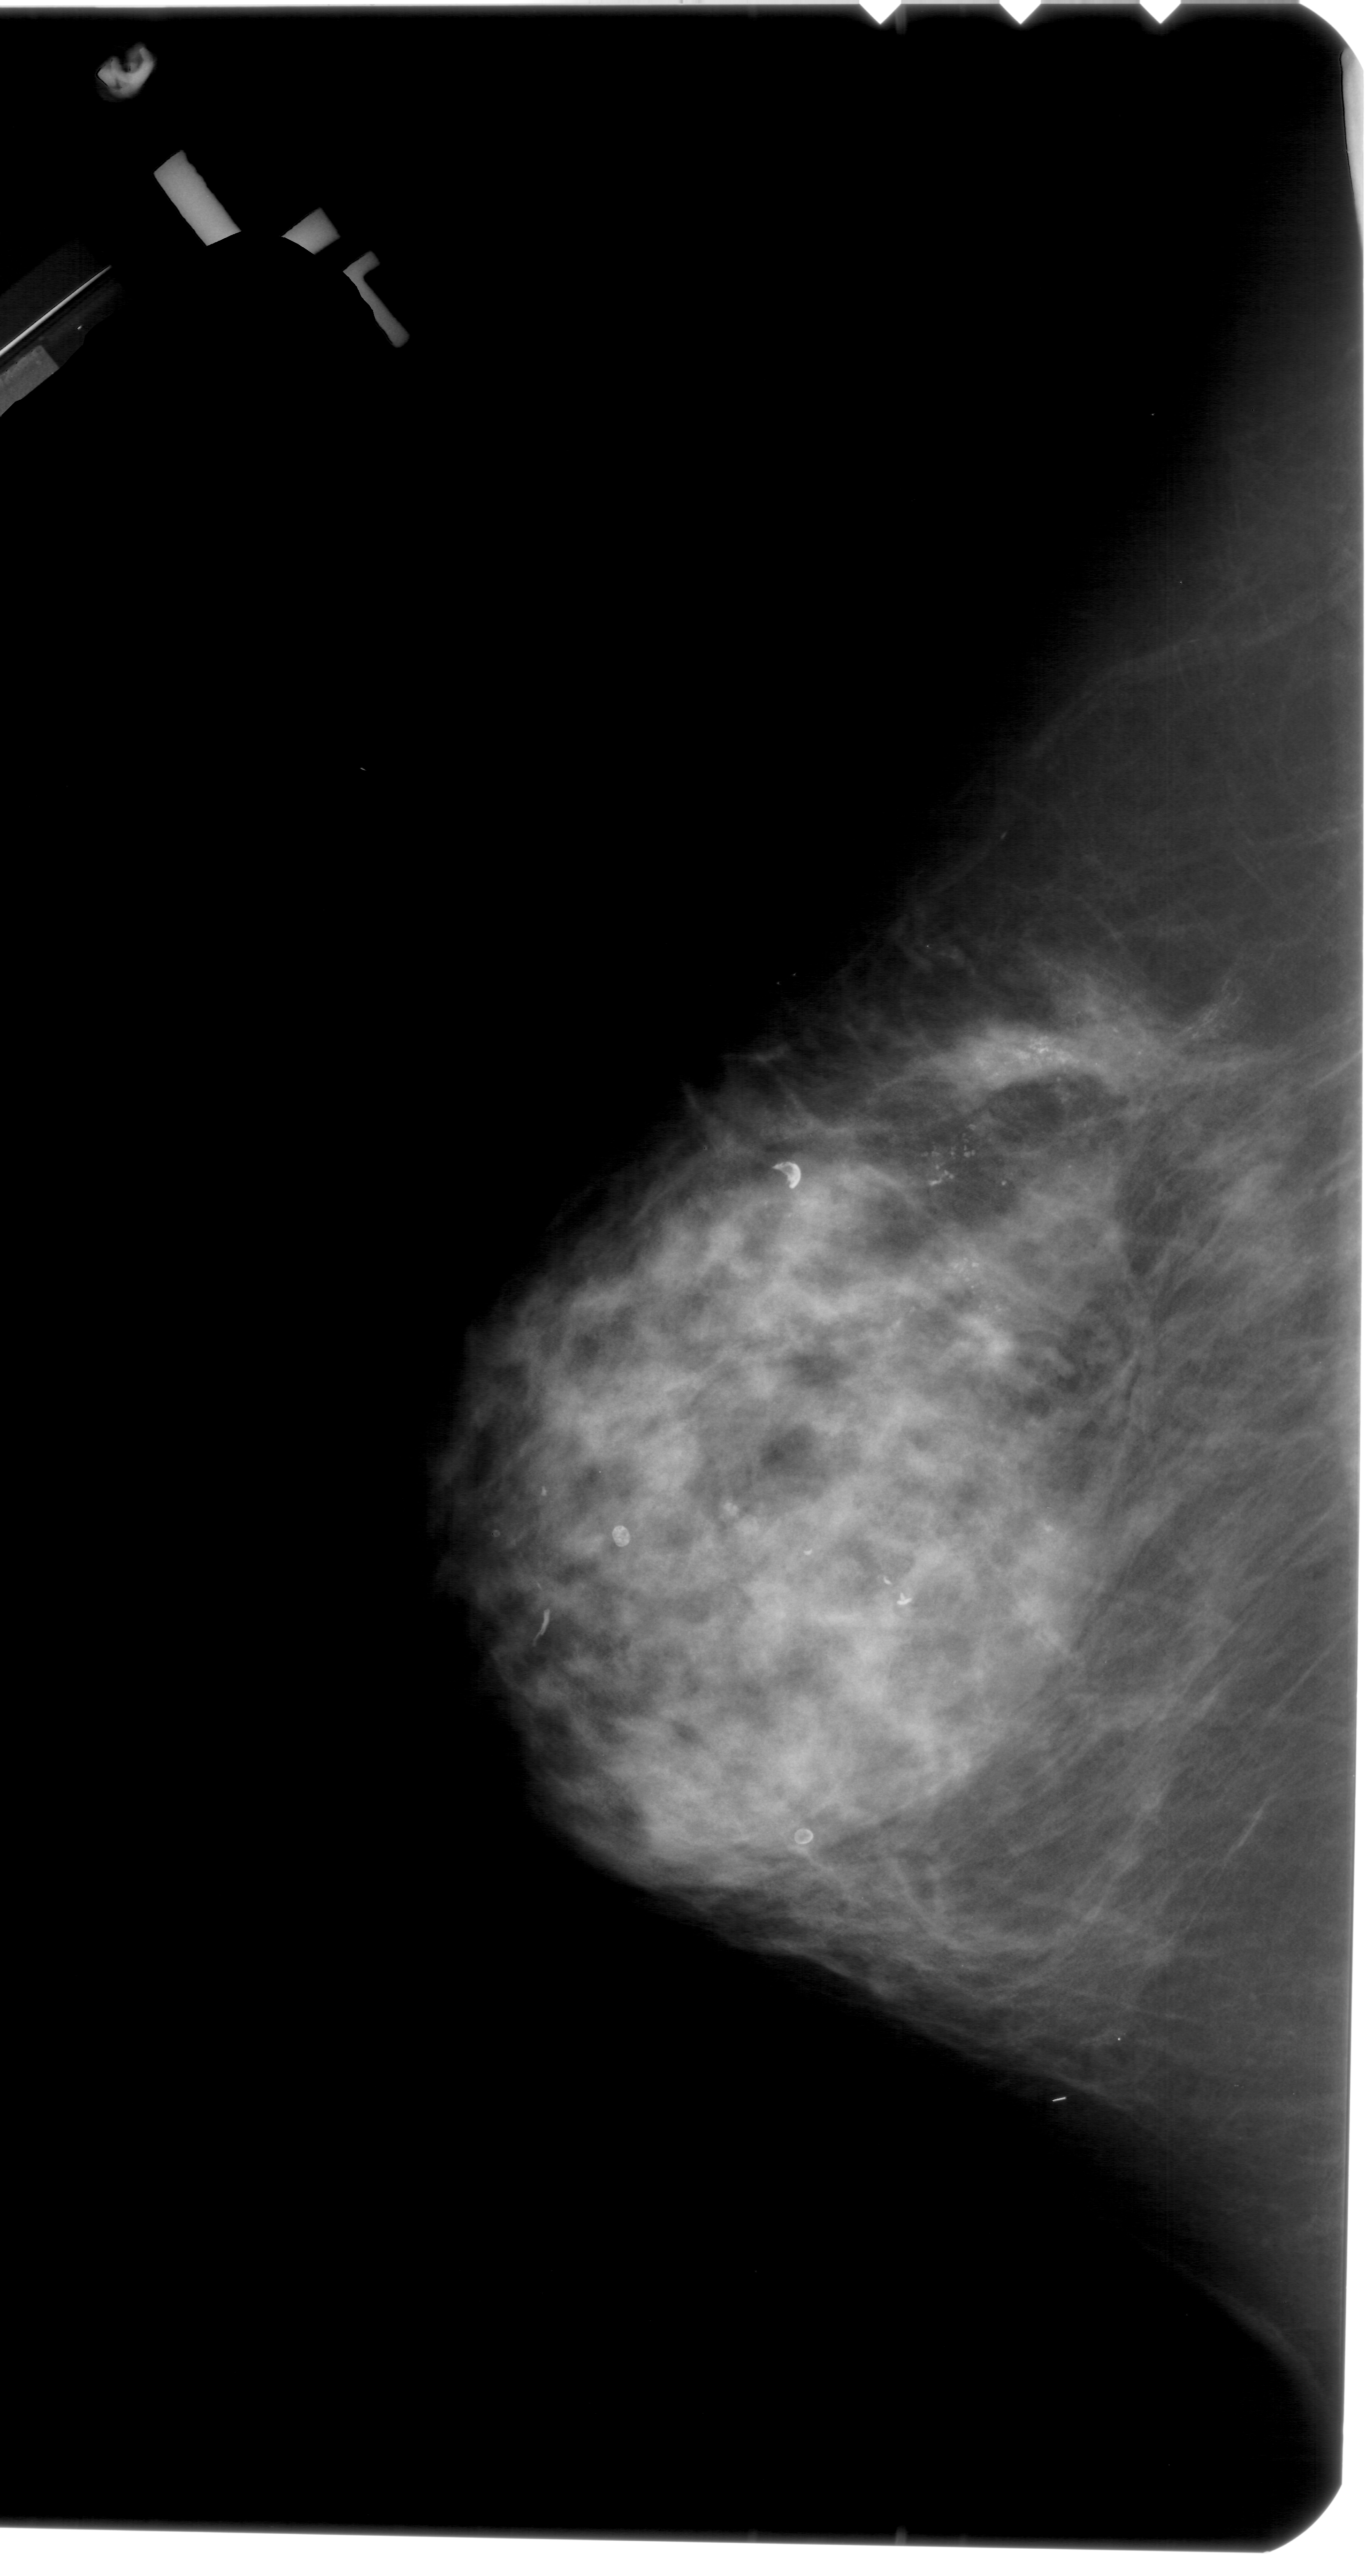
Mammogram (digitized film). Left breast. Craniocaudal (CC) view. BI-RADS breast density category 4 (scale 1–4). 1366 × 2576 image matrix.
Expert-marked regions of interest on this film, with their recorded descriptors:
- calcifications, morphology pleomorphic, distribution regional; BI-RADS assessment category 5; pathology (as recorded): malignant: bounding box <700,868,1317,1437> (left, top, right, bottom; pixels)